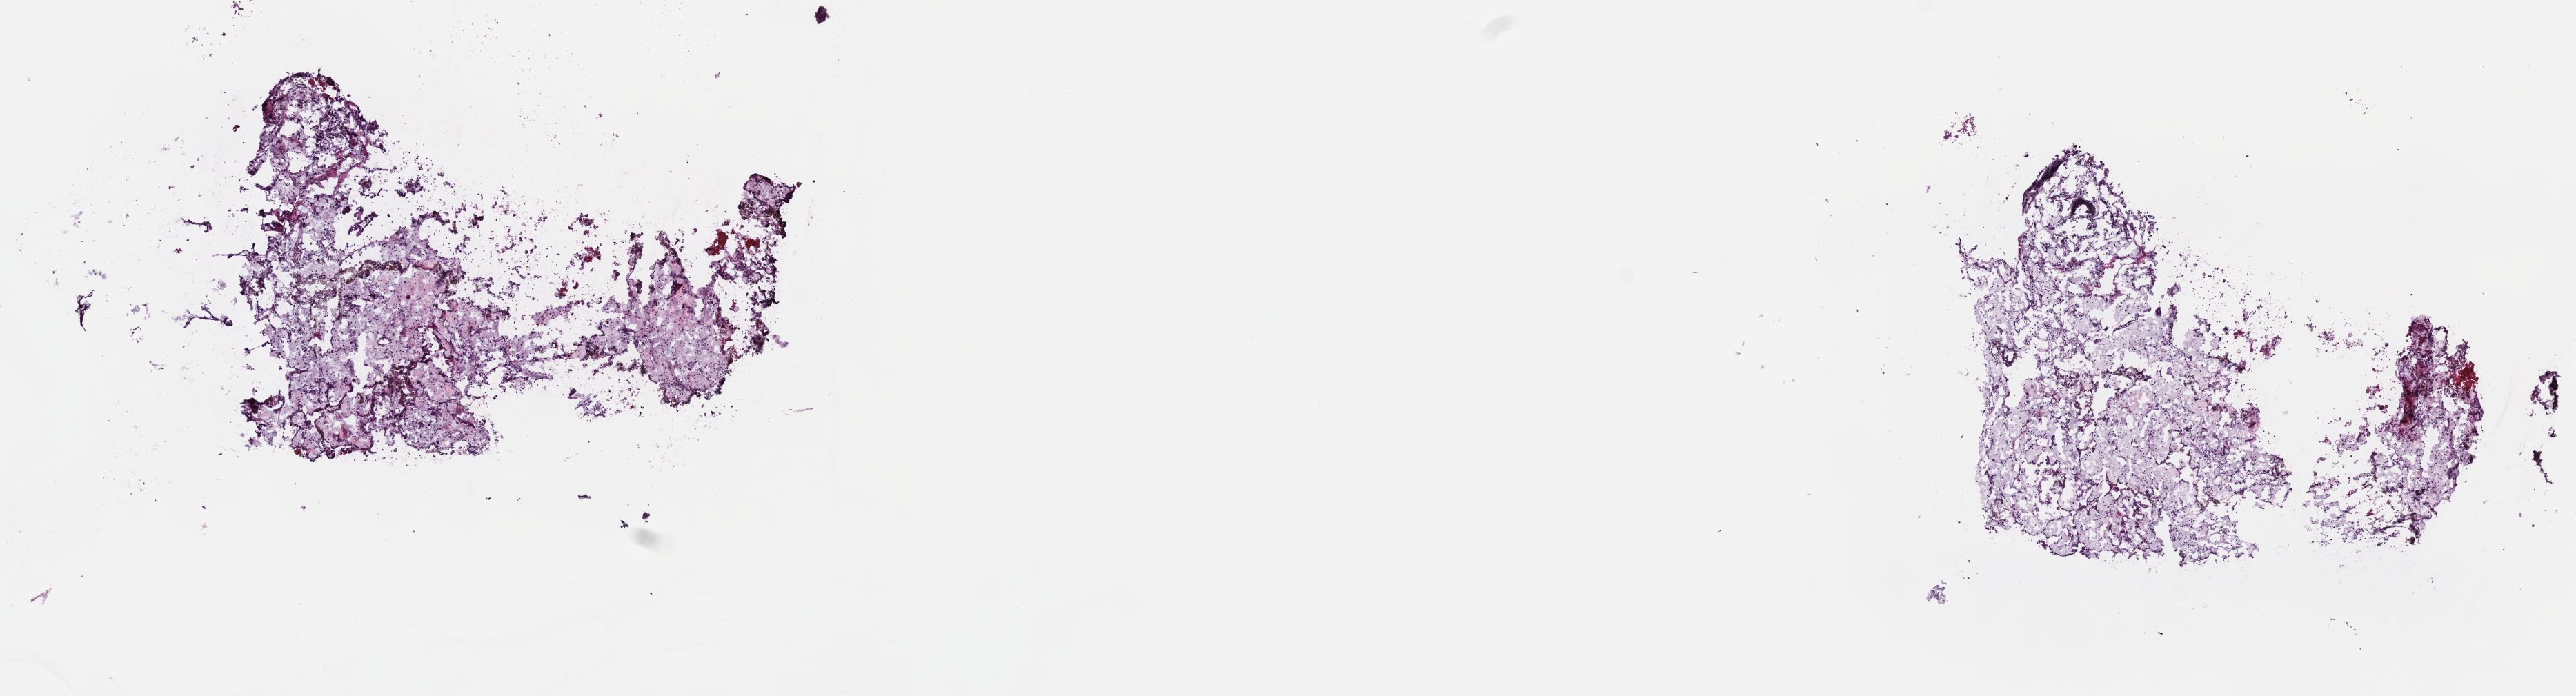
Whole-slide histology image, H&E-stained, whole scanned area (about 15.1 x 4.1 mm) shown as a low-resolution overview. Frozen section from the top of the tissue portion. Sample: primary tumour, kidney. Patient: male, age at initial diagnosis 53 years. Slide review estimates, as recorded: tumour cells 100%, tumour nuclei 60%, normal cells 0%, stromal cells 0%, necrosis 0%. Infiltration values recorded for this section: lymphocyte infiltration 2%, monocyte infiltration 15%, neutrophil infiltration 0%.
TNM: T2b NX M0. Histologic diagnosis: Papillary adenocarcinoma, NOS. AJCC pathologic stage: II. Laterality: left.